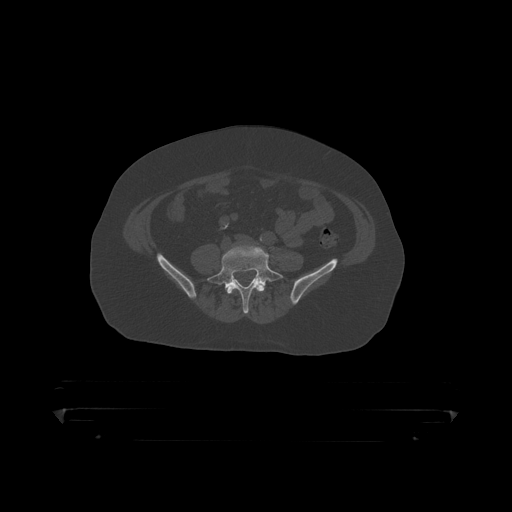
CT including the spine, one axial slice. Slice 44 of 390 in the series (ordered by position). Reconstruction kernel STANDARD. 120 kVp. Bone window (W 1800 / L 400 HU). 1.25 mm slice thickness. 512 × 512 image matrix, field of view 650 × 650 mm. Patient: male, 60 years. Case-level facts recorded for this patient, not image findings: primary cancer: prostate.
Annotated regions visible in this slice (semi-automatically segmented with operator editing):
- L4 vertebra: bounding box <227,282,265,295> (left, top, right, bottom; pixels)
- L5 vertebra: <208,246,284,314>